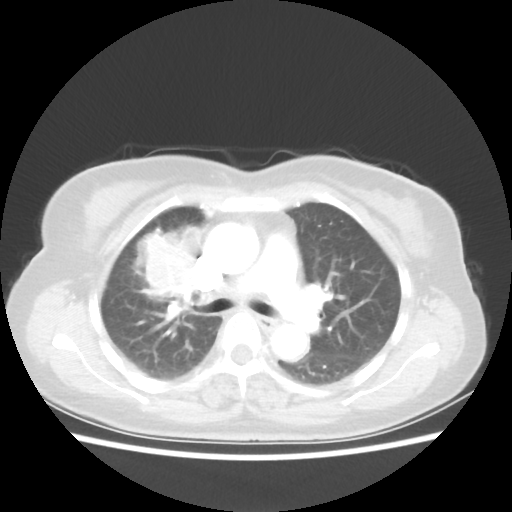
Chest CT, one axial slice; position 34 of 55 along the scan axis; lung window (W 1500 / L -600 HU); 5 mm slice thickness; 512 × 512 image matrix, field of view 337 × 337 mm. Patient: female, 62 years. From the clinical record (not read from this slice): clinical TNM (as recorded): T4 N3 M0.
Annotated regions visible in this slice (bounding box drawn by a radiologist):
- lung tumour (recorded histology: squamous cell carcinoma): box from (x=115, y=220) to (x=209, y=311) px